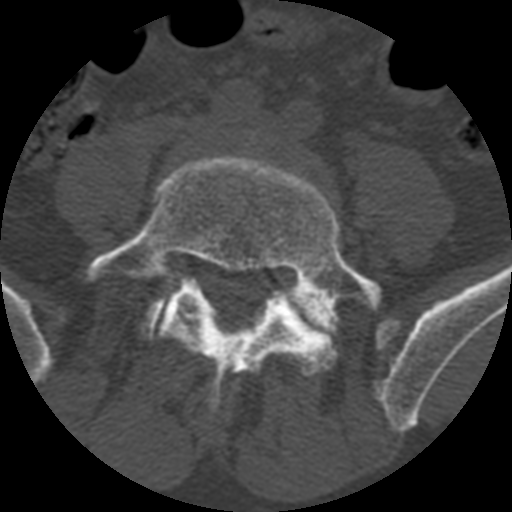
CT including the spine, one axial slice; slice 257 of 399 in the series (ordered by position); reconstruction kernel STANDARD; 120 kVp; bone window (W 1800 / L 400 HU); 1.25 mm slice thickness; 512 × 512 image matrix. Patient age 71 years. From the clinical record (not read from this slice): primary cancer: prostate.
Outlined on this slice (semi-automatically segmented with operator editing):
- L5 vertebra: box from (x=84, y=154) to (x=381, y=411) px